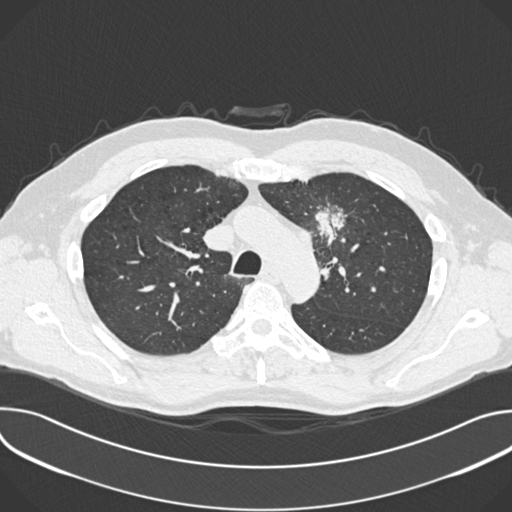
Low-dose screening chest CT, one axial slice. Position 269 of 361 along the scan axis. Reconstruction kernel B30f. Lung window (W 1500 / L -600 HU). 1 mm slice thickness. 512 × 512 image matrix, field of view 380 × 380 mm.
Structures marked on this image (expert manual segmentation):
- lesion 1 (tumor, upper lobe of left lung): bounding box [x1, y1, x2, y2] px = [316, 209, 344, 240]